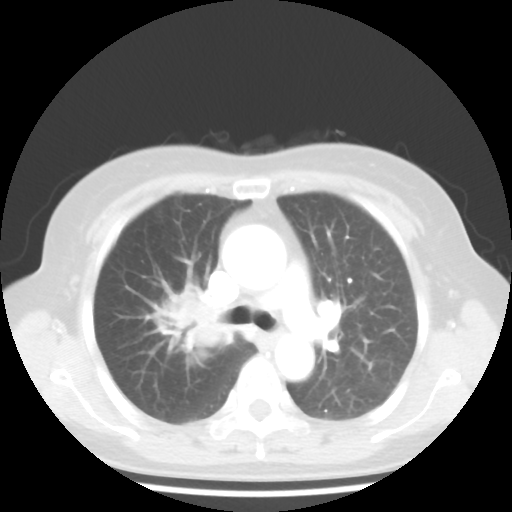
Chest CT, one axial slice; slice 28 of 44 in the series (ordered by position); reconstruction kernel STANDARD; 100 kVp; lung window (W 1500 / L -600 HU); 5 mm slice thickness; 512 × 512 image matrix, field of view 316 × 316 mm. Female patient, age 62 years. From the clinical record (not read from this slice): clinical TNM (as recorded): T3 N0 M0; histopathological grade: G3.
Structures marked on this image (rectangle marked by the reading radiologist):
- lung tumour (recorded histology: small cell carcinoma): bounding box <142,277,238,357> (left, top, right, bottom; pixels)